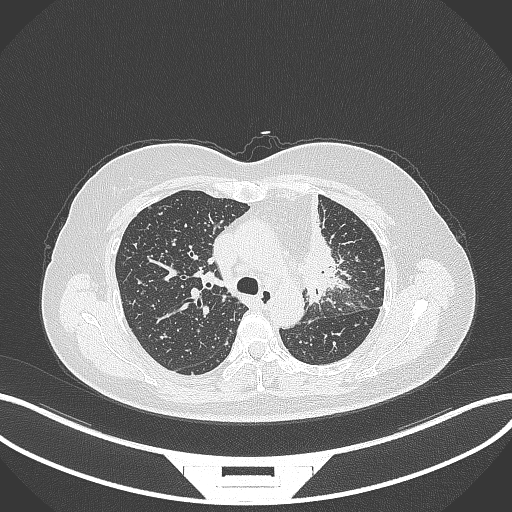
Chest CT, one axial slice; position 229 of 348 along the scan axis; 120 kVp; lung window (W 1500 / L -600 HU); 1 mm slice thickness; 512 × 512 image matrix, field of view 400 × 400 mm. Patient: female, 49 years. Case-level facts recorded for this patient, not image findings: clinical TNM (as recorded): T1c N0 M1.
Outlined on this slice (rectangle marked by the reading radiologist):
- lung tumour (recorded histology: adenocarcinoma): bounding box (x1, y1, x2, y2) in pixels: (297, 194, 352, 304)